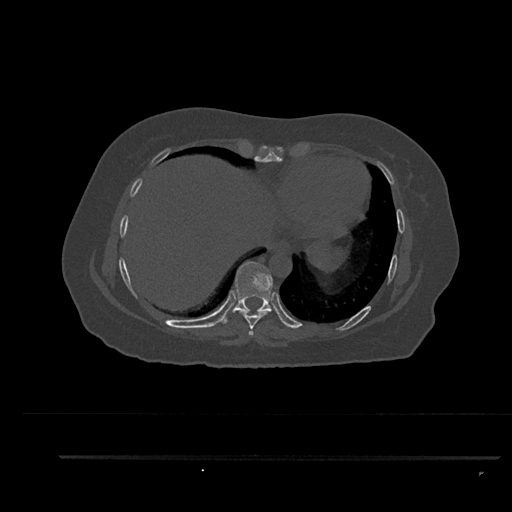
CT including the spine, one axial slice; slice 437 of 797 in the series (ordered by position); reconstruction kernel Br40s/3; 120 kVp; bone window (W 1800 / L 400 HU); 0.5 mm slice thickness; 512 × 512 image matrix. Patient: female, 44 years. Case-level facts recorded for this patient, not image findings: primary cancer: renal; vertebrae with lytic lesions (as recorded): L1.
Outlined on this slice (semi-automatic segmentation, software-assisted and operator-edited):
- T7 vertebra: bounding box [x1, y1, x2, y2] px = [249, 331, 254, 336]
- T8 vertebra: [236, 309, 269, 330]
- T9 vertebra: [224, 261, 273, 324]